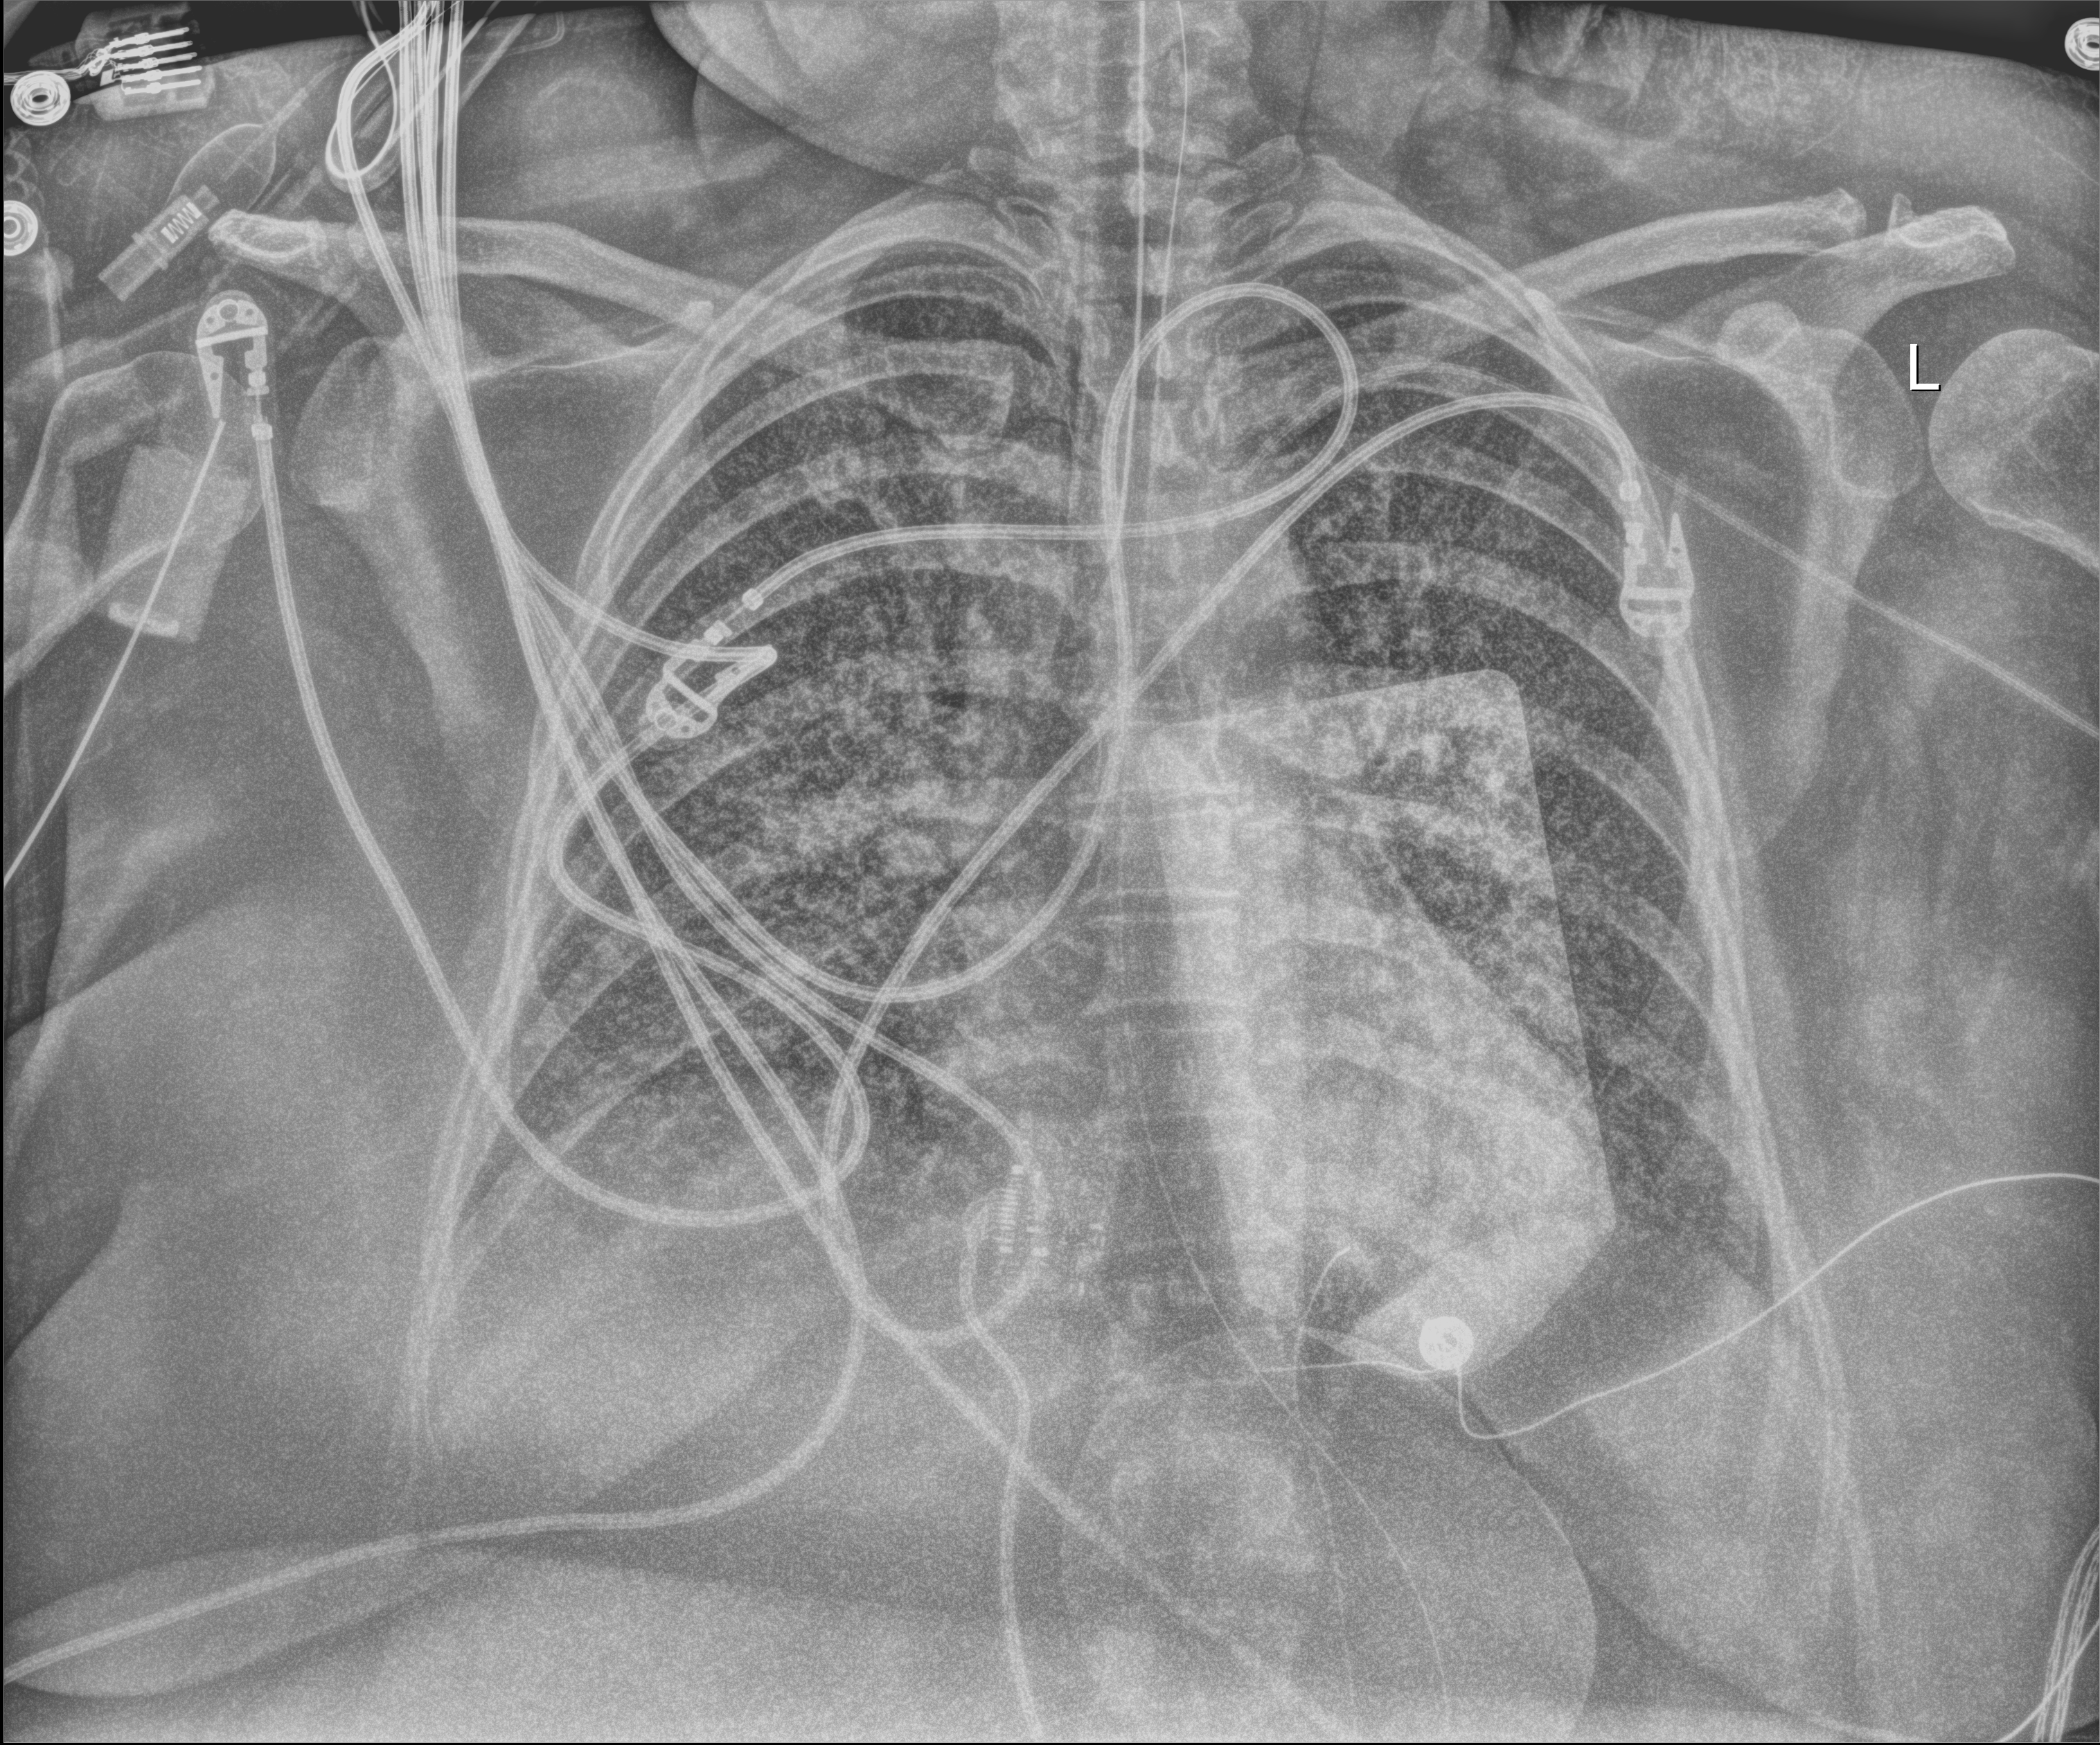
Bedside chest radiograph (digital radiography); anteroposterior (AP) projection. Female patient hospitalised with COVID-19, age 18–59 years.
Hospital-stay facts (about this admission, not read from this image; timing relative to this image not recorded): length of hospital stay: 95 days.